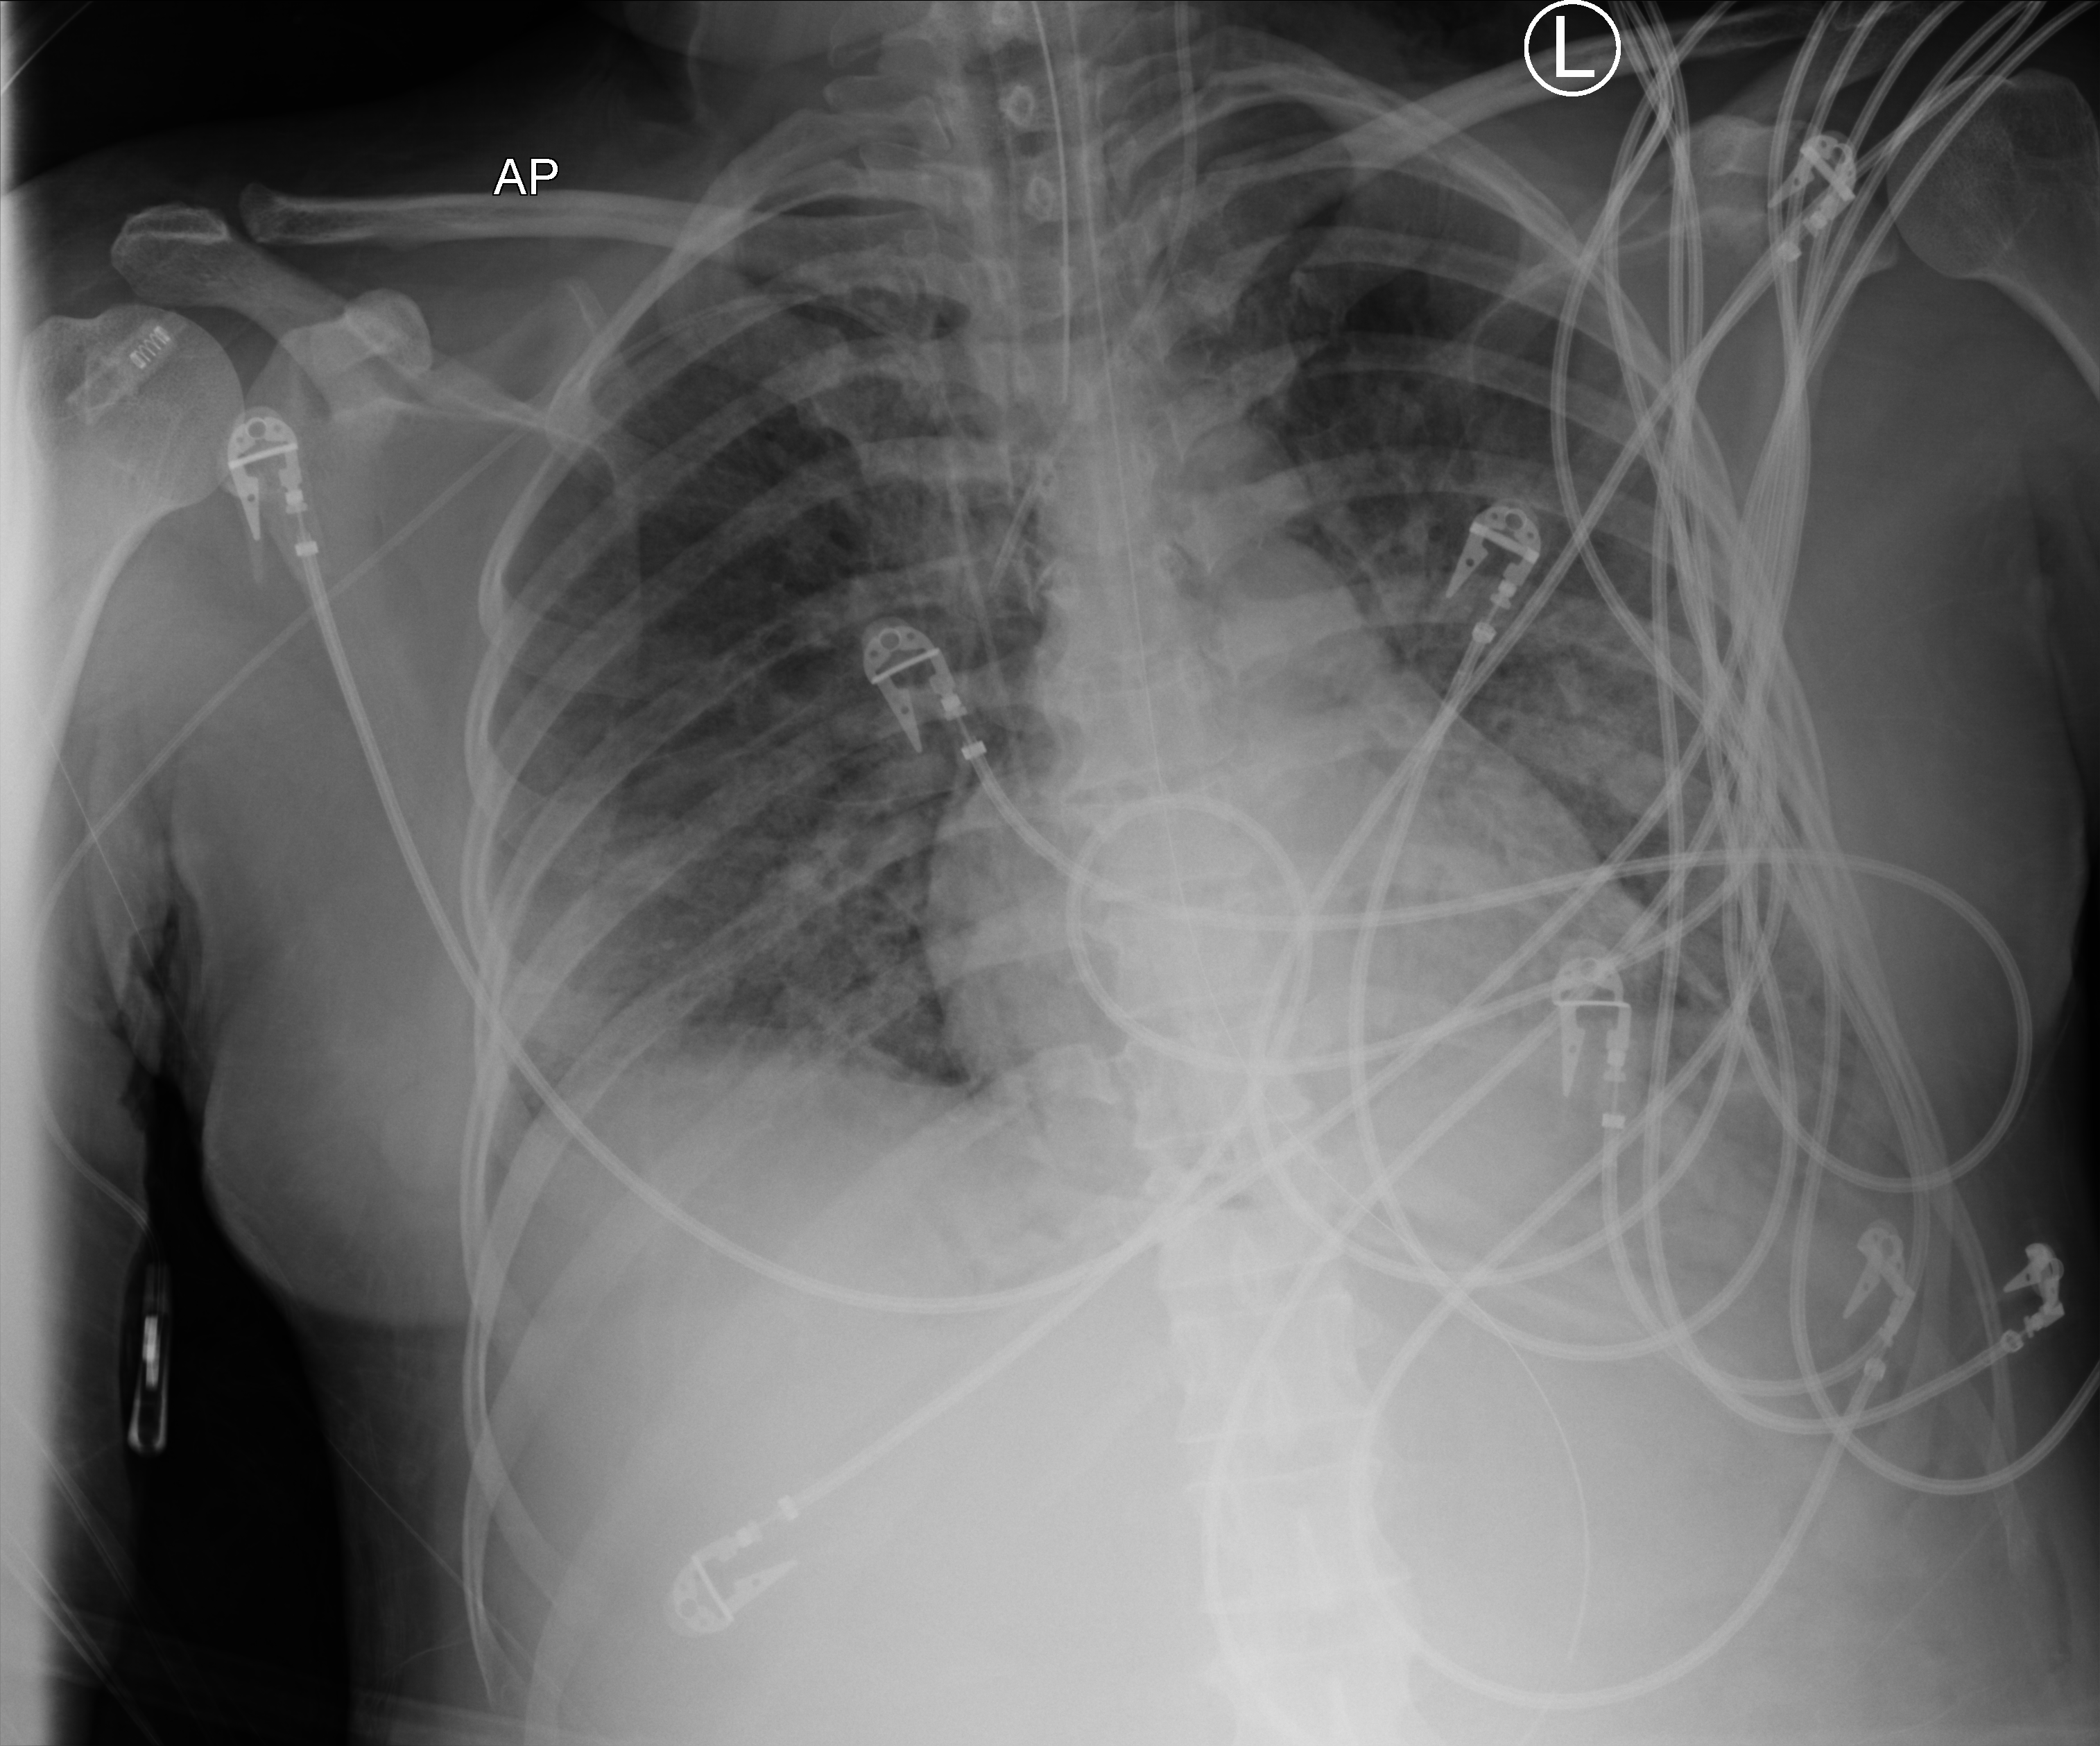
Chest X-ray (portable); anteroposterior (AP) projection. Patient hospitalised with COVID-19; female, aged 18–59 years.
From the hospital-stay record, not from the radiograph (when in the stay this image was taken is not recorded): mechanically ventilated during this hospital stay: yes.